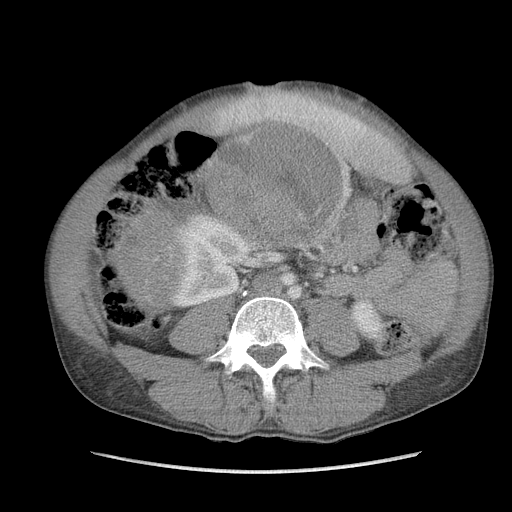
Contrast-enhanced abdominal CT, one axial slice; slice 43 of 115 in the series (ordered by position); soft-tissue window (W 400 / L 40 HU); 5 mm slice thickness; 512 × 512 image matrix, field of view 360 × 360 mm. Male patient. From the clinical record (not read from this slice): diagnosis: adrenocortical carcinoma; tumour side: right adrenal; Ki-67 index: 13 %; stage (as recorded): 3.
Annotated regions visible in this slice (semi-automatic segmentation, software-assisted and operator-edited):
- mass: bounding box [x1, y1, x2, y2] px = [119, 127, 340, 301]